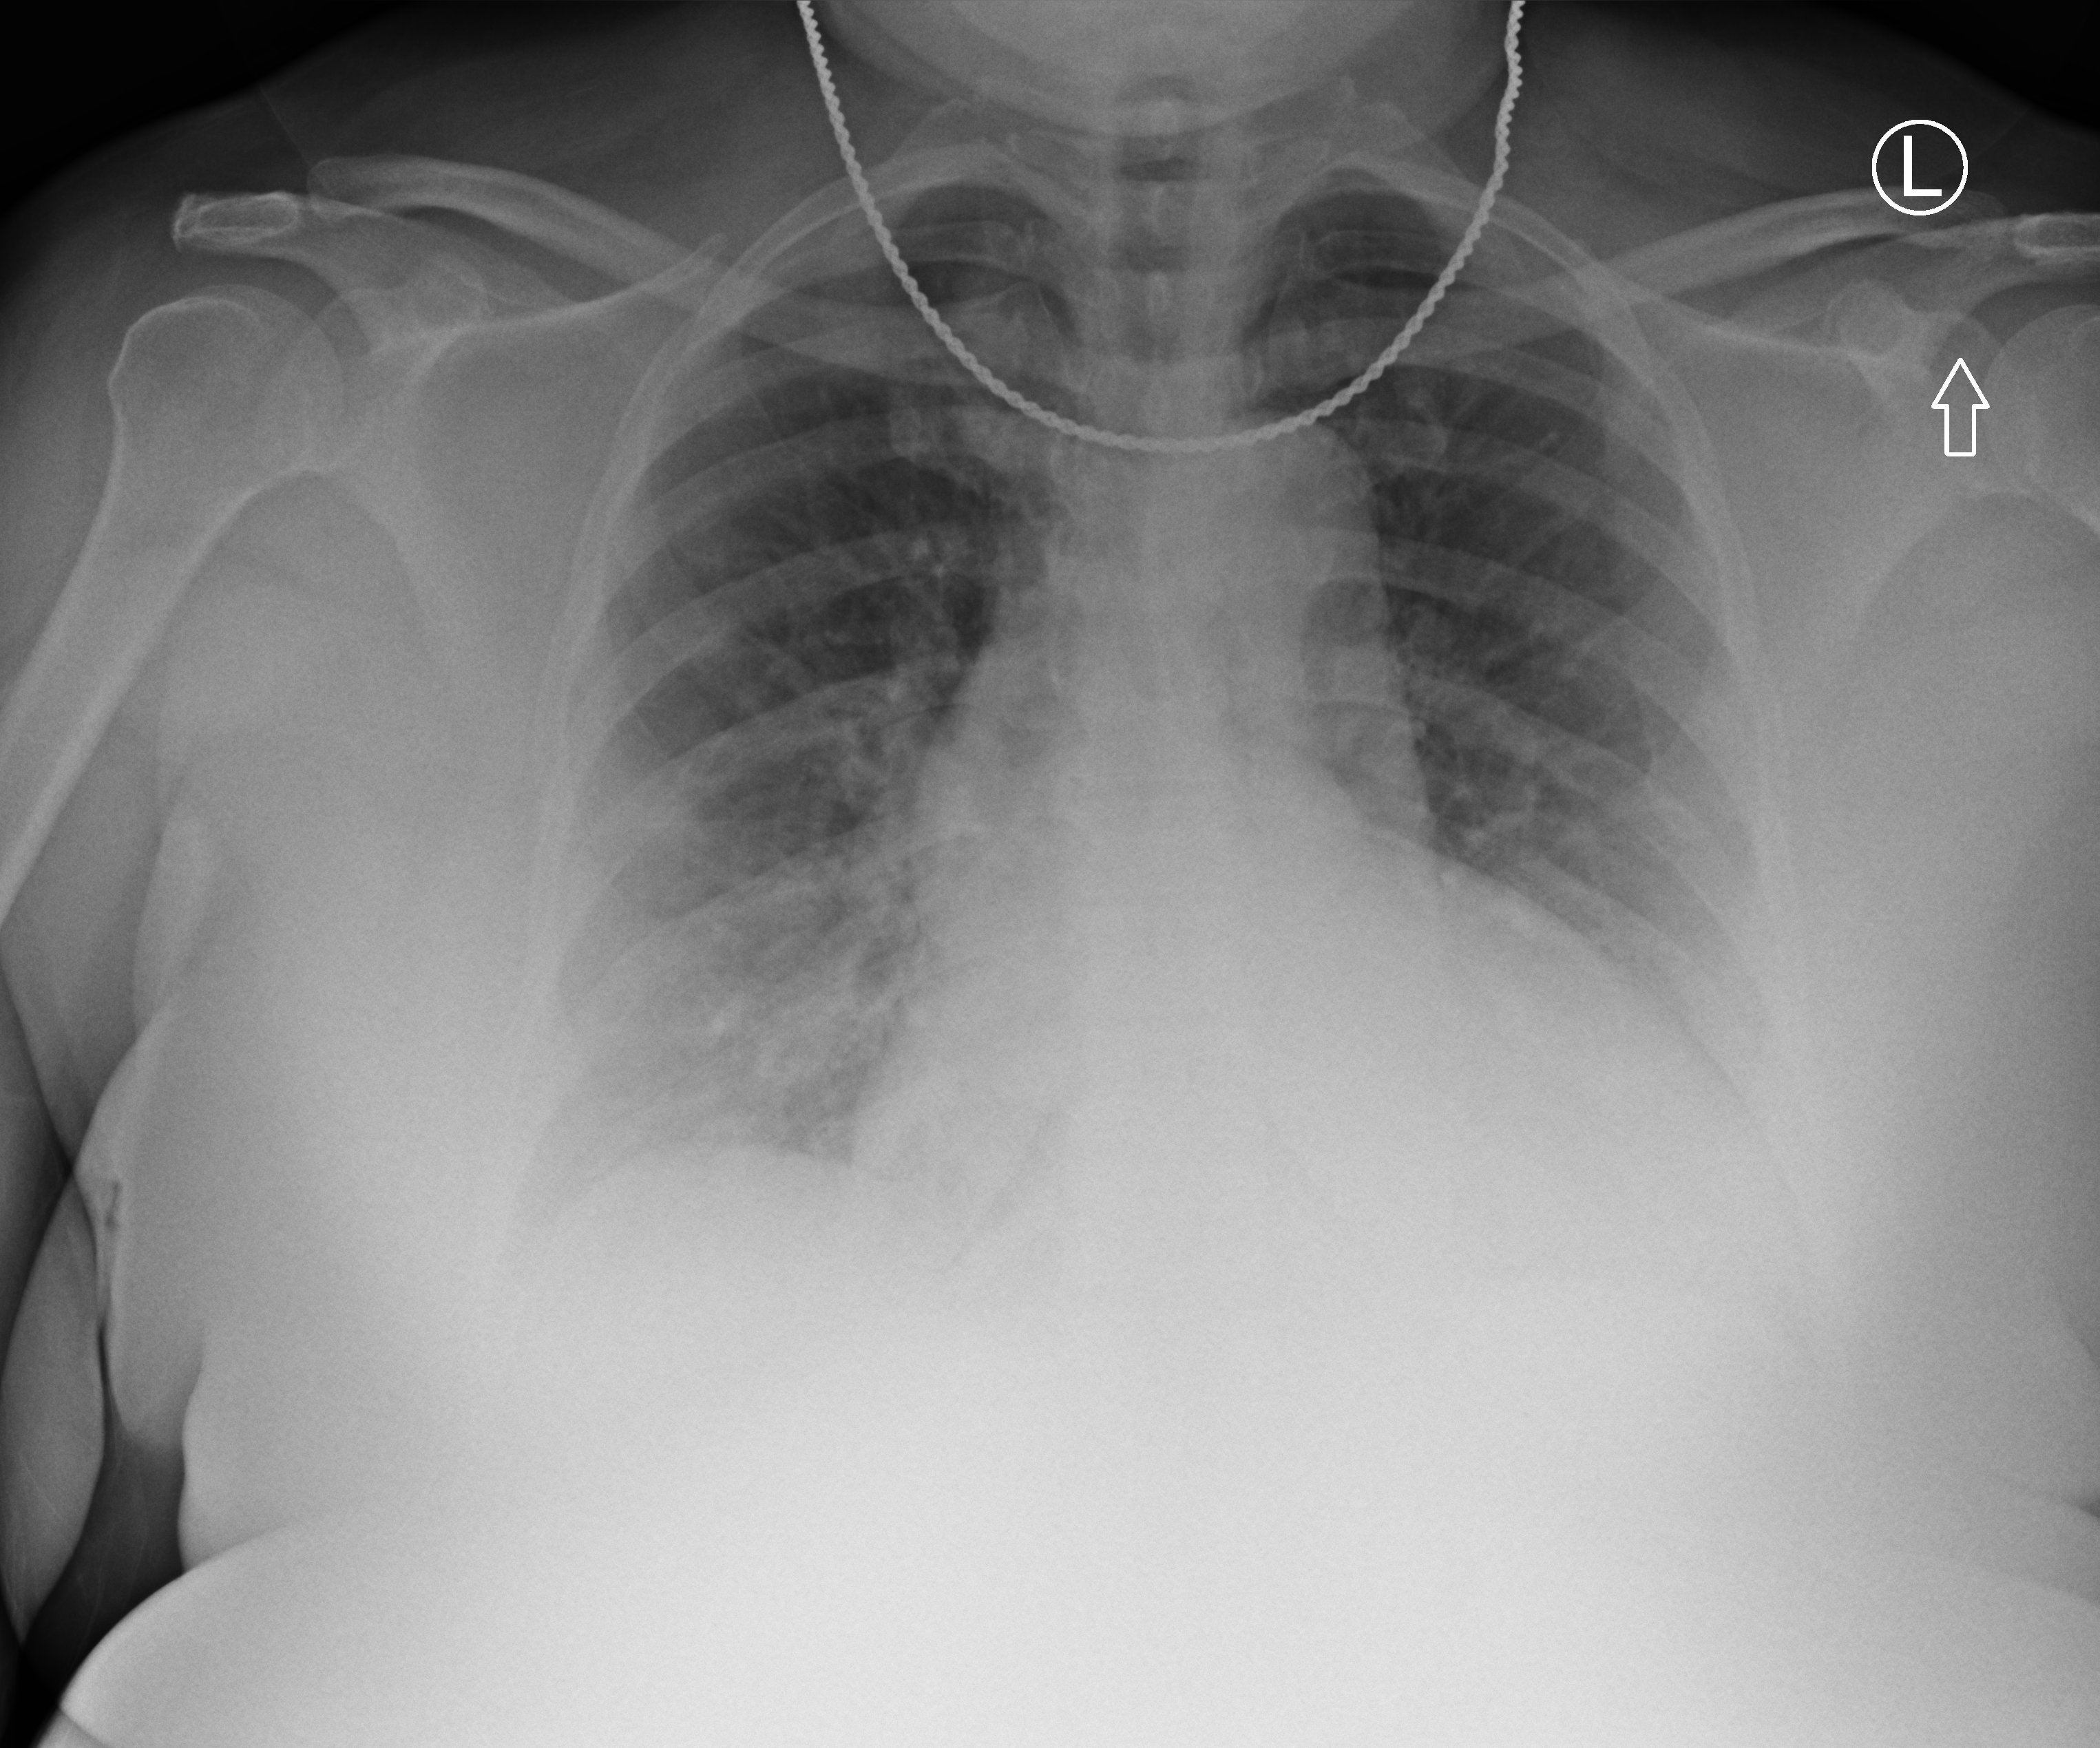
Portable chest radiograph; anteroposterior (AP) projection. Patient hospitalised with COVID-19; female, aged 60–74 years.
Admission-level facts for this patient (not findings on this image; timing relative to this image not recorded):
- admitted to intensive care during this hospital stay: yes
- other chronic lung disease (admission record): no